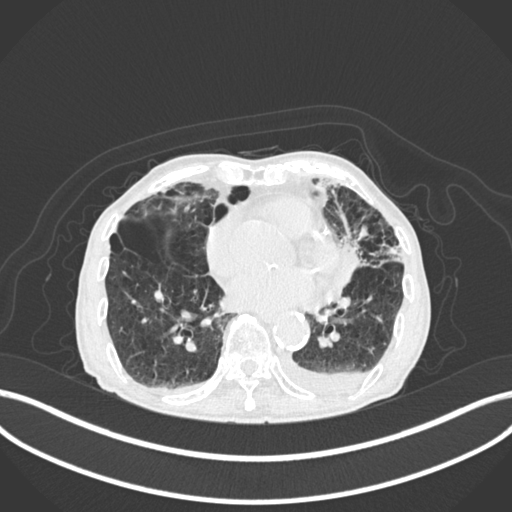
Chest CT, one axial slice; slice 78 of 400 in the series (ordered by position); reconstruction kernel B30f; 120 kVp; lung window (W 1500 / L -600 HU); 512 × 512 image matrix, field of view 400 × 400 mm. Male patient, age 90 years or older. From the clinical record (not read from this slice): clinical TNM (as recorded): T2b N1 M0.
Structures marked on this image (bounding box drawn by a radiologist):
- lung tumour (recorded histology: squamous cell carcinoma): bounding box (x1, y1, x2, y2) in pixels: (340, 230, 365, 300)